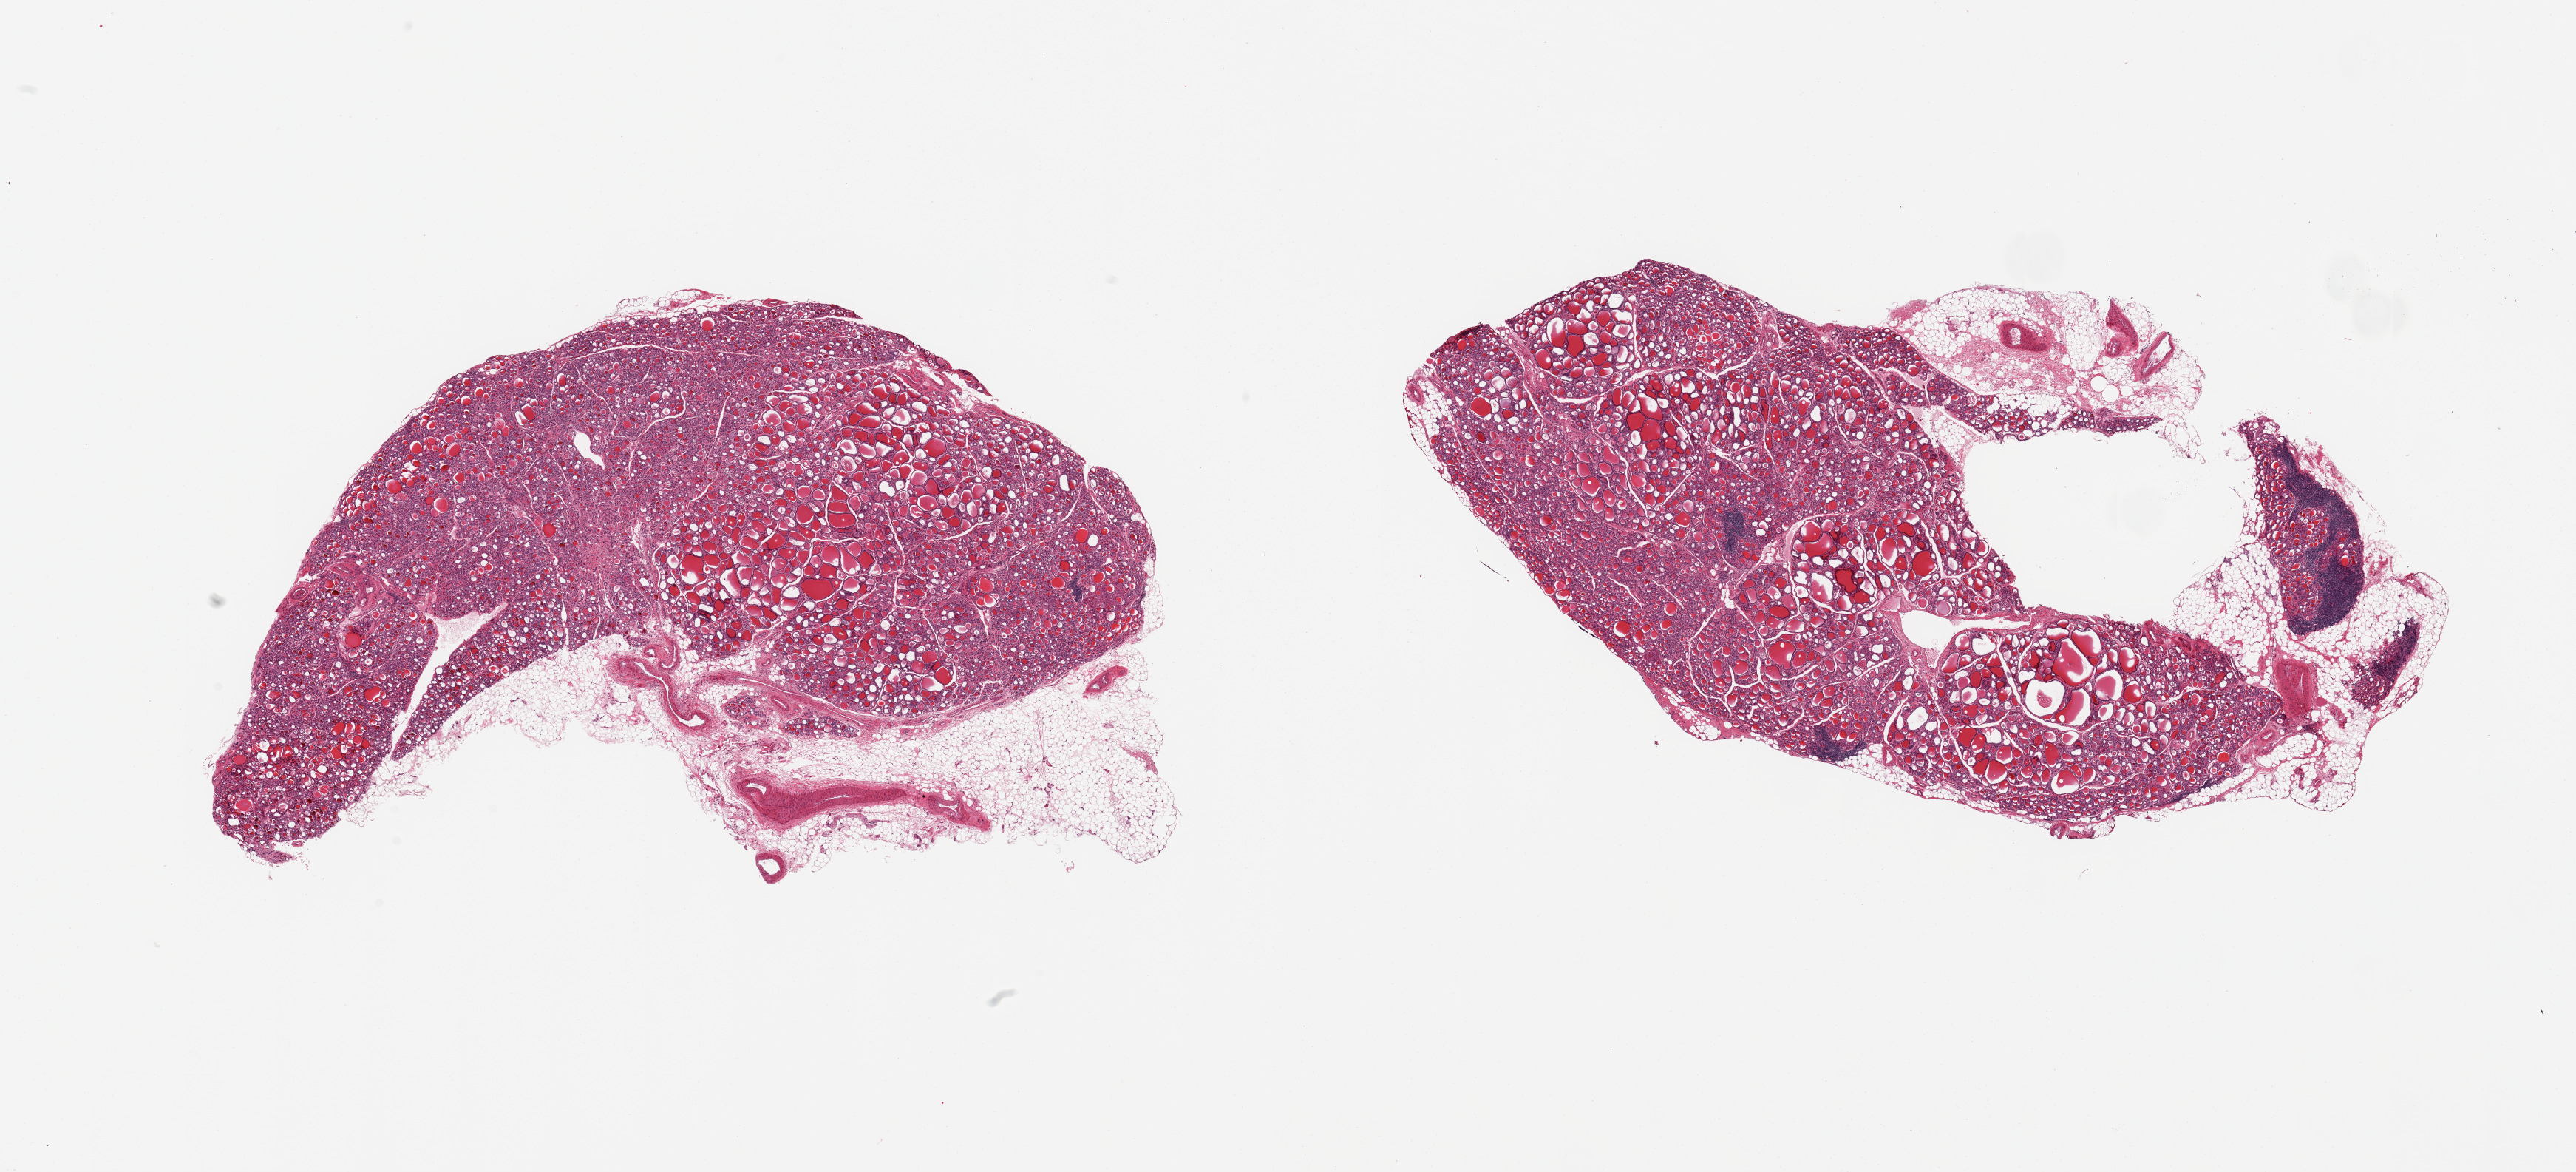
Haematoxylin and eosin whole-slide image, low-resolution overview of the scanned area, about 27.6 x 12.5 mm (acquisition: 20x scan). PAXgene-fixed, paraffin-embedded tissue. Sampled site (target tissue): thyroid. Donor tissue sample. Female donor.
Reviewer comment on this tissue sample: 2 pieces, adherent rim of fat up to ~1mm, patchy Hashimoto thyroiditis, mild.